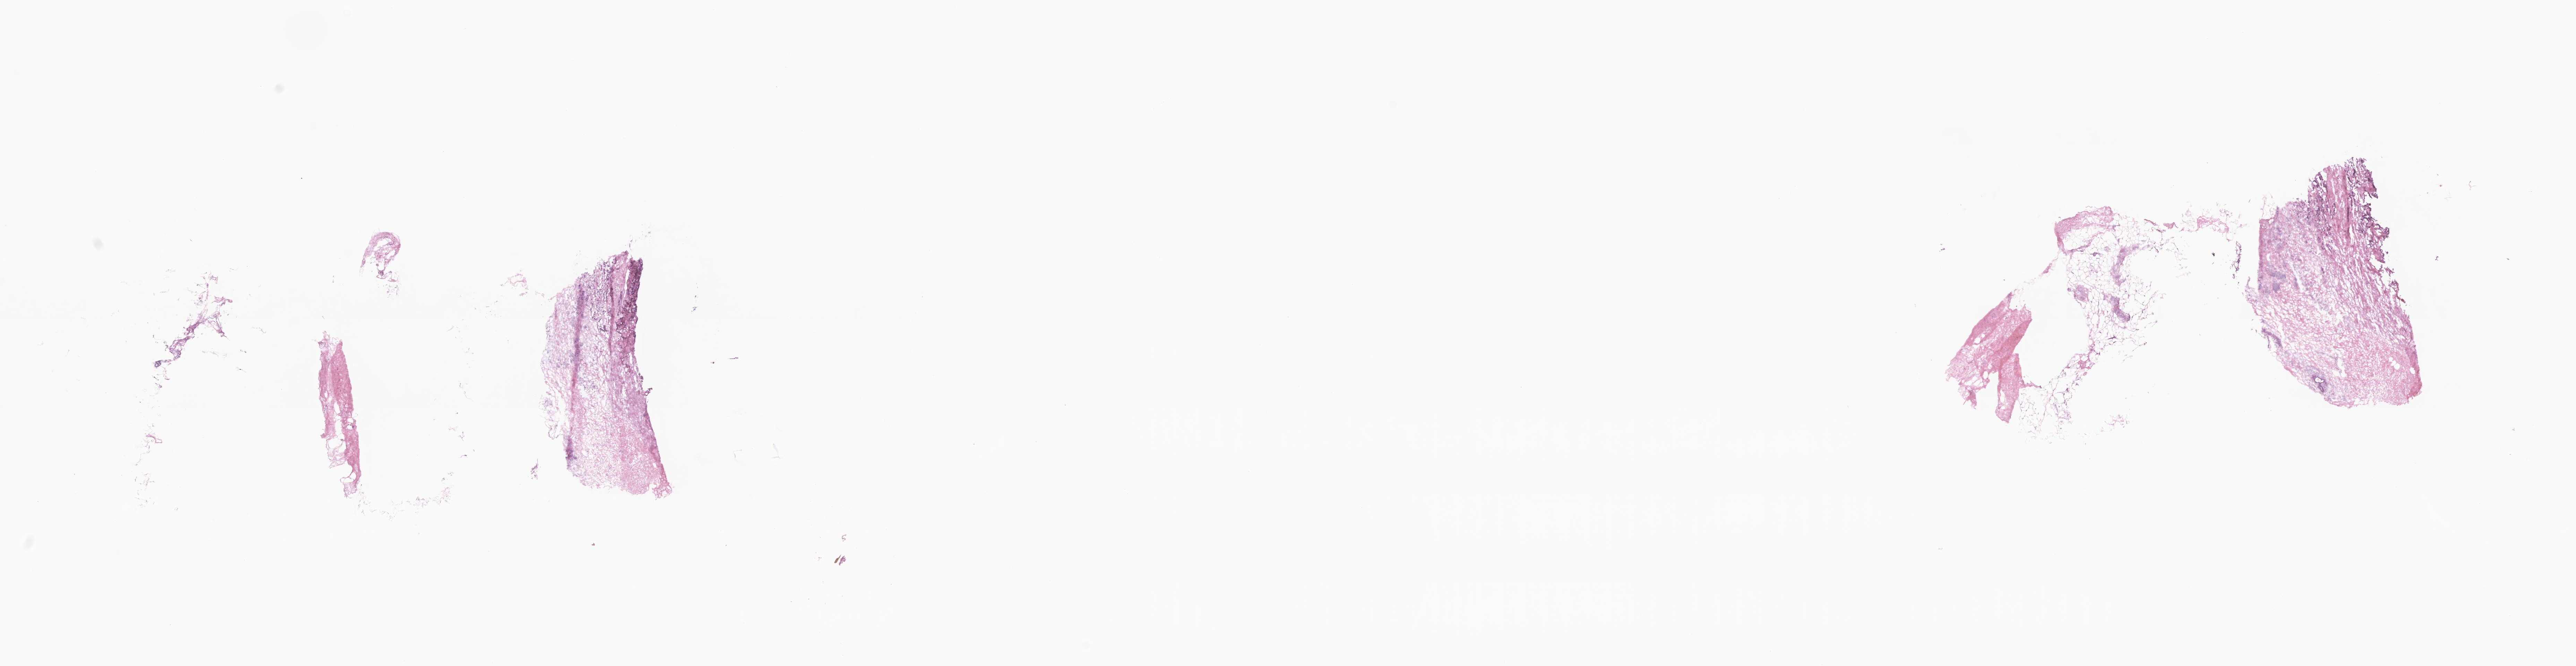
H&E whole-slide image — low-resolution overview of the scanned area, about 31.3 x 8.1 mm. Cryosection. Primary tumor. Site: breast (right). Patient: female, age at initial diagnosis 76 years. Pathologist review of this section (percent, as recorded): tumor cells 60%, tumor nuclei 60%, stromal cells 40%, necrosis 0%, normal cells 0%. Inflammatory infiltration, as recorded: lymphocyte infiltration 2%, monocyte infiltration 1%, neutrophil infiltration 4%.
Section: bottom of the tissue portion. Diagnosis: Infiltrating duct carcinoma, NOS.